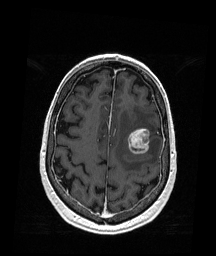
Brain MRI from a brain-tumour surgery series, one axial slice. Position 55 of 176 along the scan axis. T1-weighted post-contrast. 1 mm slice thickness. 216 × 256 image matrix. Case-level facts recorded for this patient, not image findings: histopathology: Metastatic Melanoma.
Annotated regions visible in this slice (manually delineated by an expert):
- tumour: bounding box [x1, y1, x2, y2] px = [127, 128, 151, 155]